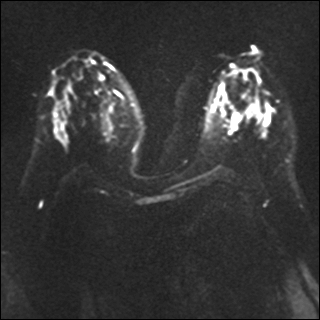
Breast MRI, one axial slice; position 18 of 41 along the scan axis; diffusion-weighted series; image 2 of 4 stored at this slice position (different b-values; order by instance number); 1.5 T; 4 mm slice thickness; 320 × 320 image matrix, field of view 340 × 340 mm. Female patient.
Structures marked on this image (expert manual segmentation):
- tumour on diffusion-weighted imaging: box from (x=248, y=105) to (x=260, y=115) px